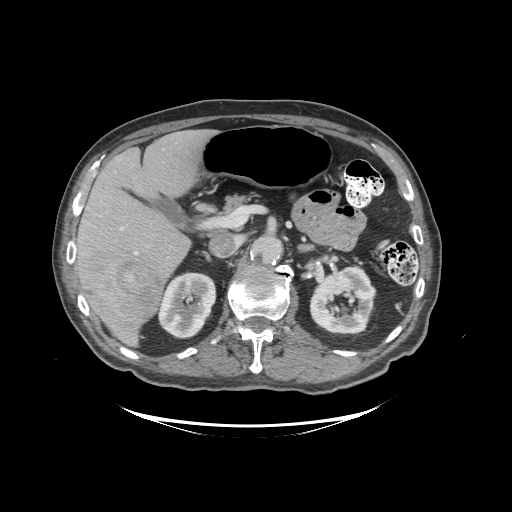
Contrast-enhanced abdominal CT (liver protocol), one axial slice; slice 54 of 99 in the series (ordered by position); 140 kVp; soft-tissue window (W 400 / L 40 HU); 2.5 mm slice thickness; 512 × 512 image matrix, field of view 460 × 460 mm. From the clinical record (not read from this slice): diagnosis: hepatocellular carcinoma (patient treated with transarterial chemoembolisation; whether this scan precedes or follows treatment is not stated here); TNM stage (as recorded): Stage-I; Child-Pugh class: A; tumour nodularity: uninodular.
Annotated regions visible in this slice (semi-automatically segmented with operator editing):
- liver parenchyma outside the tumour (the mass and vessels are separate outlines, so this box may not span the whole liver): bounding box <72,130,214,344> (left, top, right, bottom; pixels)
- mass: <89,255,163,328>
- liver vessels: <73,227,138,257>